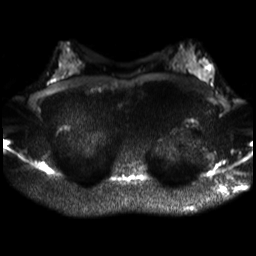
Breast MRI, one axial slice; slice 19 of 30 in the series (ordered by position); diffusion-weighted series; image 2 of 4 stored at this slice position (different b-values; order by instance number); 3 T; 256 × 256 image matrix, field of view 320 × 320 mm. Female patient.
Outlined on this slice (outlined manually by an expert reader):
- tumour on diffusion-weighted imaging: box from (x=201, y=68) to (x=212, y=76) px